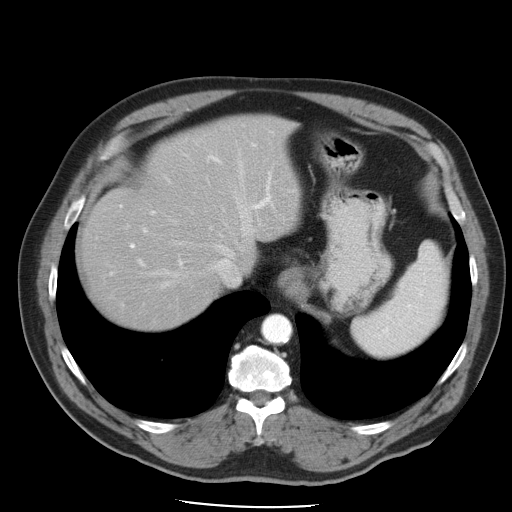
Contrast-enhanced abdominal CT, one axial slice; slice 39 of 49 in the series (ordered by position); intravenous contrast given; soft-tissue window (W 400 / L 40 HU); 5 mm slice thickness; 512 × 512 image matrix. Male patient, age 68 years. From the clinical record (not read from this slice): diagnosis: colorectal cancer liver metastases, imaged before liver resection.
Annotated regions visible in this slice (manually delineated by an expert):
- hepatic veins: box from (x=149, y=204) to (x=256, y=289) px
- liver: (x=81, y=116)–(x=302, y=329)
- planned liver remnant (the part of the liver to remain after resection): (x=81, y=116)–(x=301, y=329)
- portal vein (with intrahepatic branches): (x=111, y=132)–(x=293, y=276)